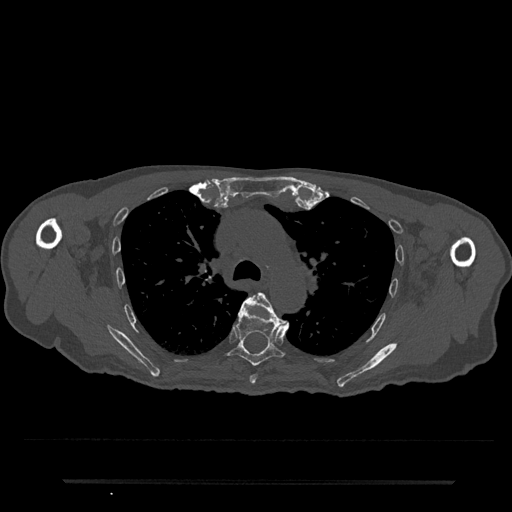
CT including the spine, one axial slice. Position 541 of 797 along the scan axis. 120 kVp. Bone window (W 1800 / L 400 HU). 0.5 mm slice thickness. 512 × 512 image matrix. Male patient, age 74 years. From the clinical record (not read from this slice): primary cancer: prostate.
Structures marked on this image (semi-automatically segmented with operator editing):
- T5 vertebra: bounding box <239,293,289,385> (left, top, right, bottom; pixels)
- T6 vertebra: <227,299,285,366>